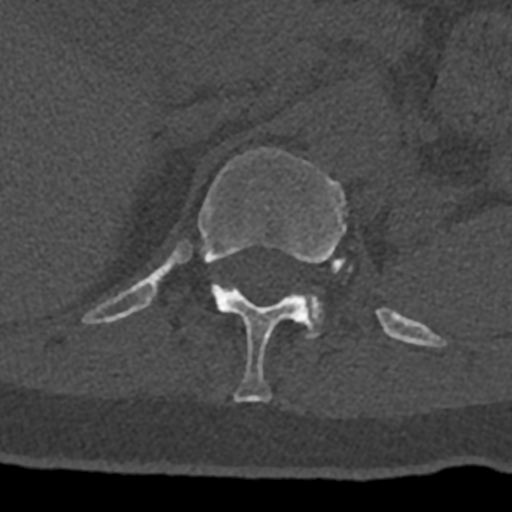
CT including the spine, one axial slice; slice 484 of 797 in the series (ordered by position); reconstruction kernel Br40s/3; 120 kVp; bone window (W 1800 / L 400 HU); 0.5 mm slice thickness; 512 × 512 image matrix, field of view 160 × 160 mm. Patient: male, 74 years. Case-level facts recorded for this patient, not image findings: primary cancer: renal; vertebrae with lytic lesions (as recorded): T10, L1, L2, L3, L4, L5.
Structures marked on this image (semi-automatically segmented with operator editing):
- L1 vertebra: bounding box <305,293,323,338> (left, top, right, bottom; pixels)
- T12 vertebra: <82,148,432,403>